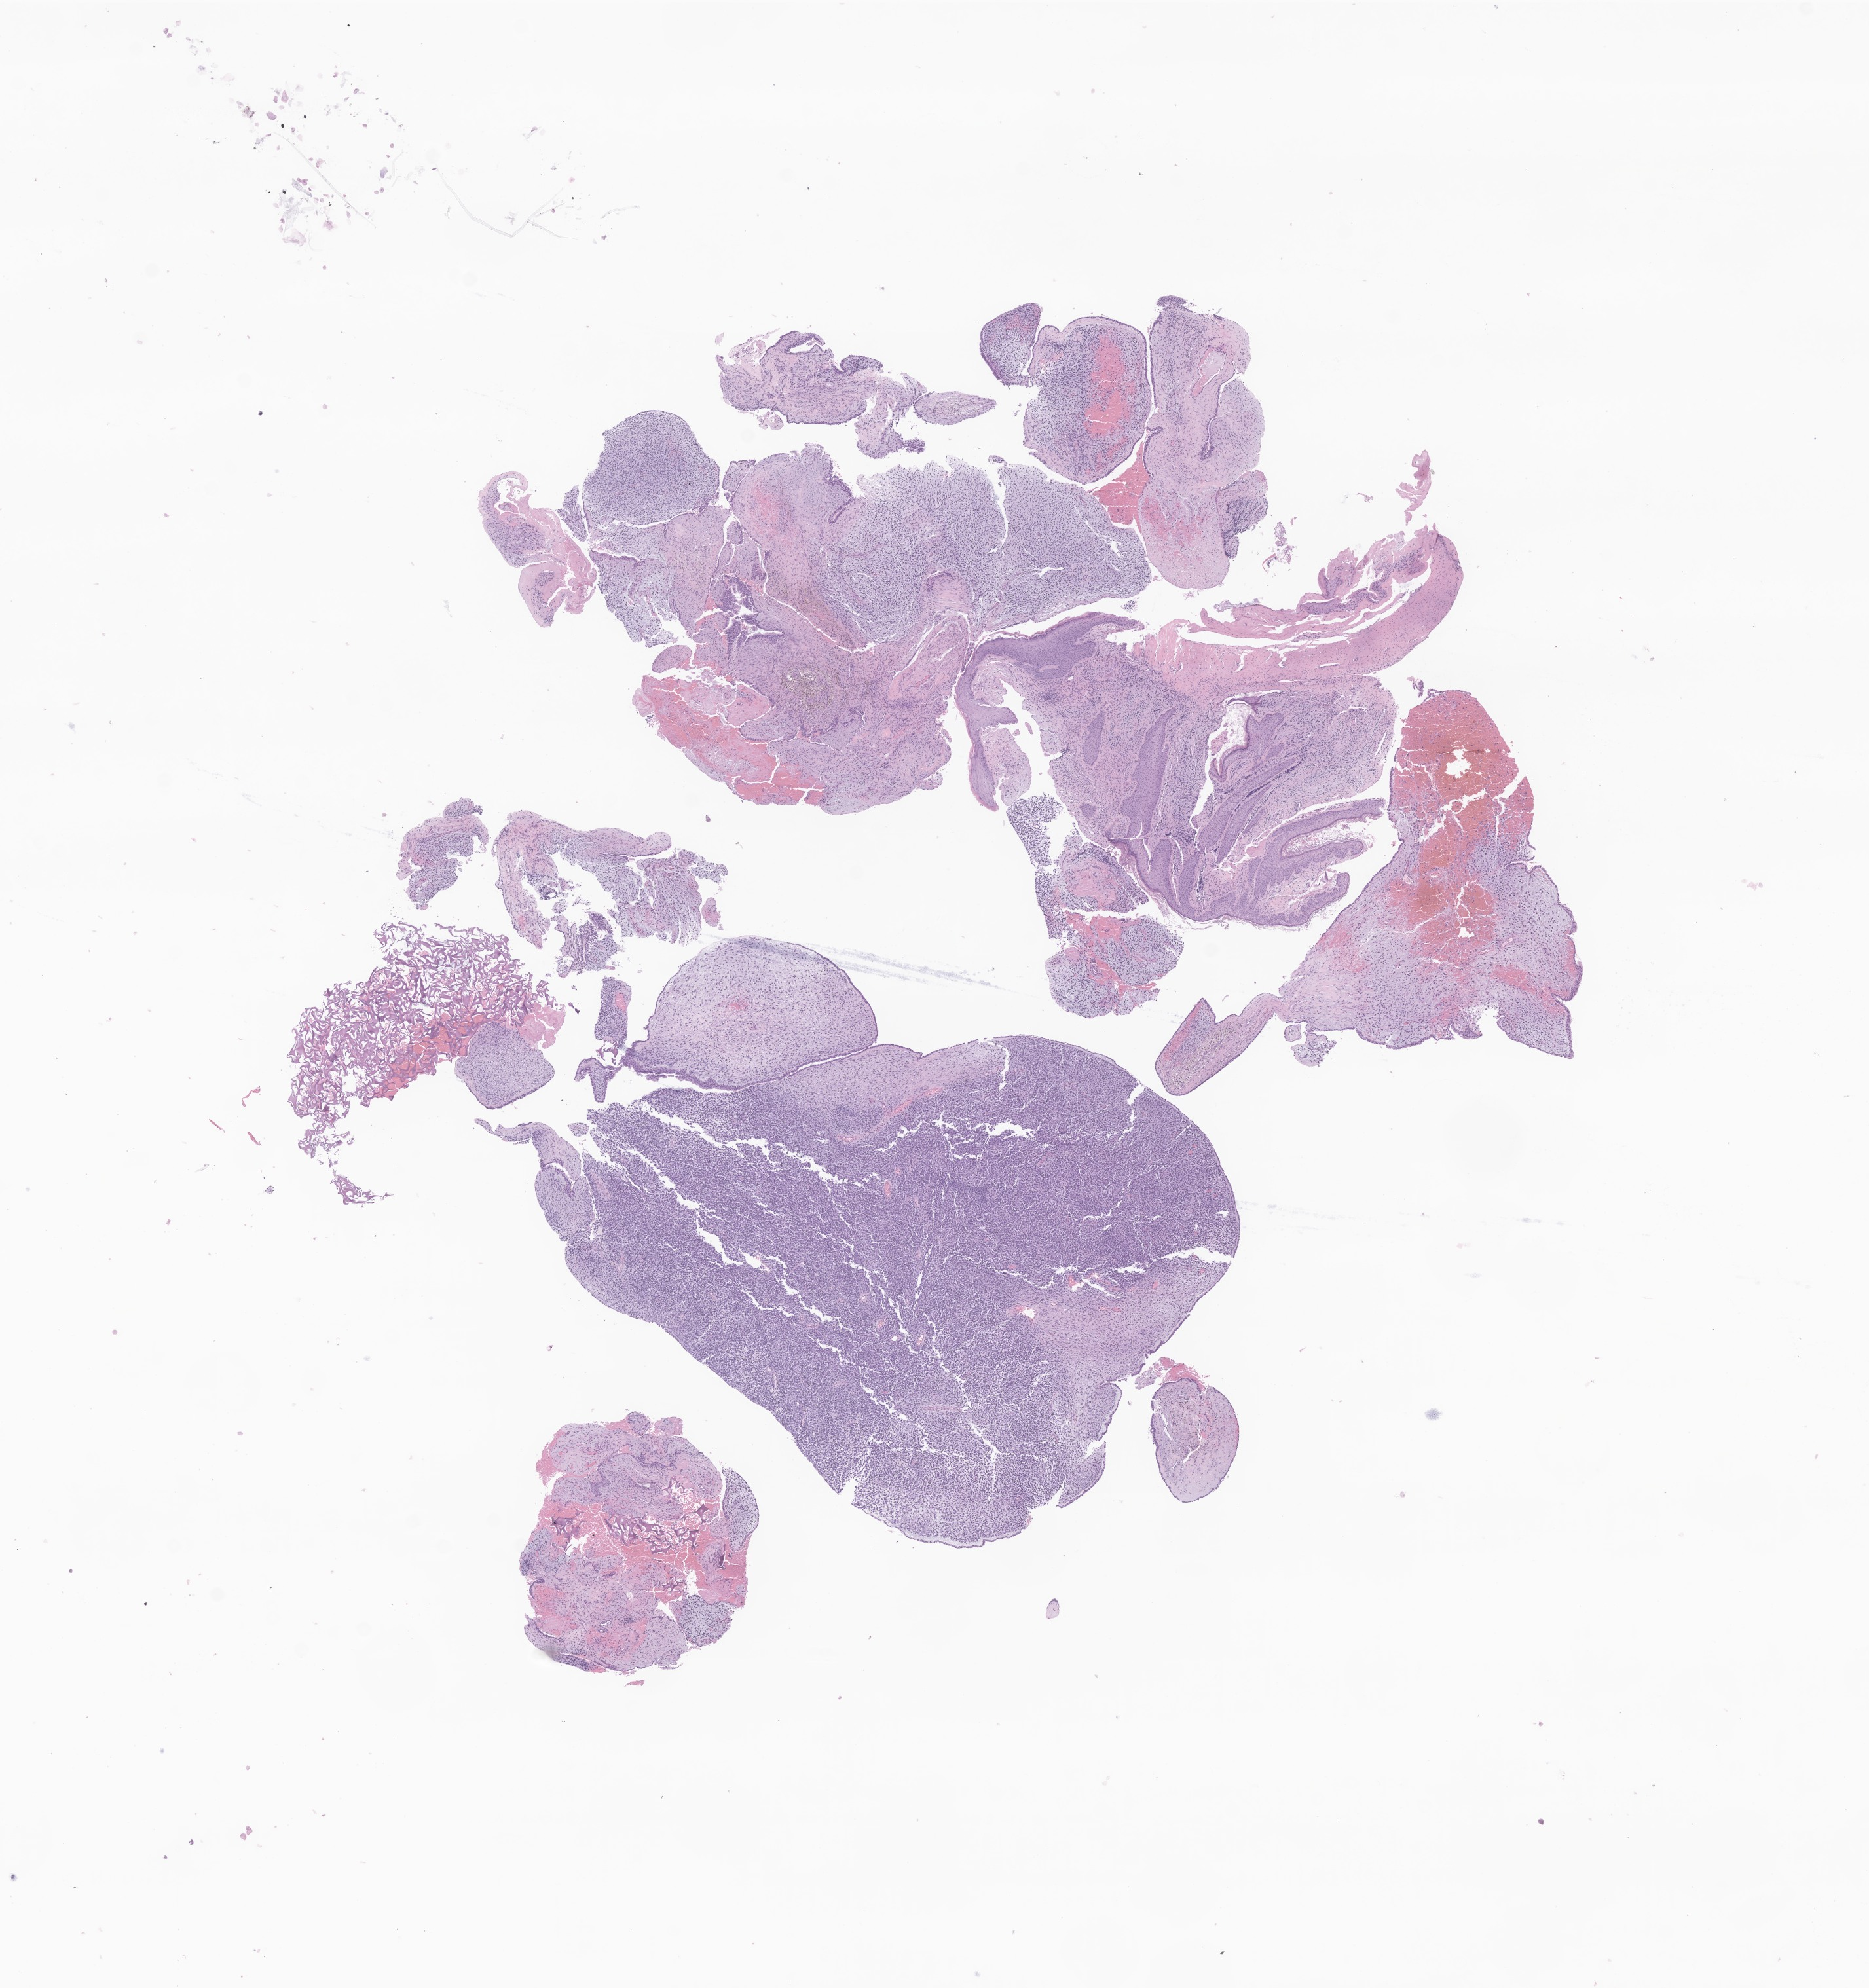
Whole-slide image, hematoxylin and eosin (H&E) stain of tumor tissue from the middle ear — shown as a low-resolution overview of the whole scanned area (about 12.0 x 12.8 mm); formalin-fixed, paraffin-embedded (FFPE) tissue. Male patient, age 74 months (6 years 2 months).
Diagnosis: Embryonal rhabdomyosarcoma, NOS.